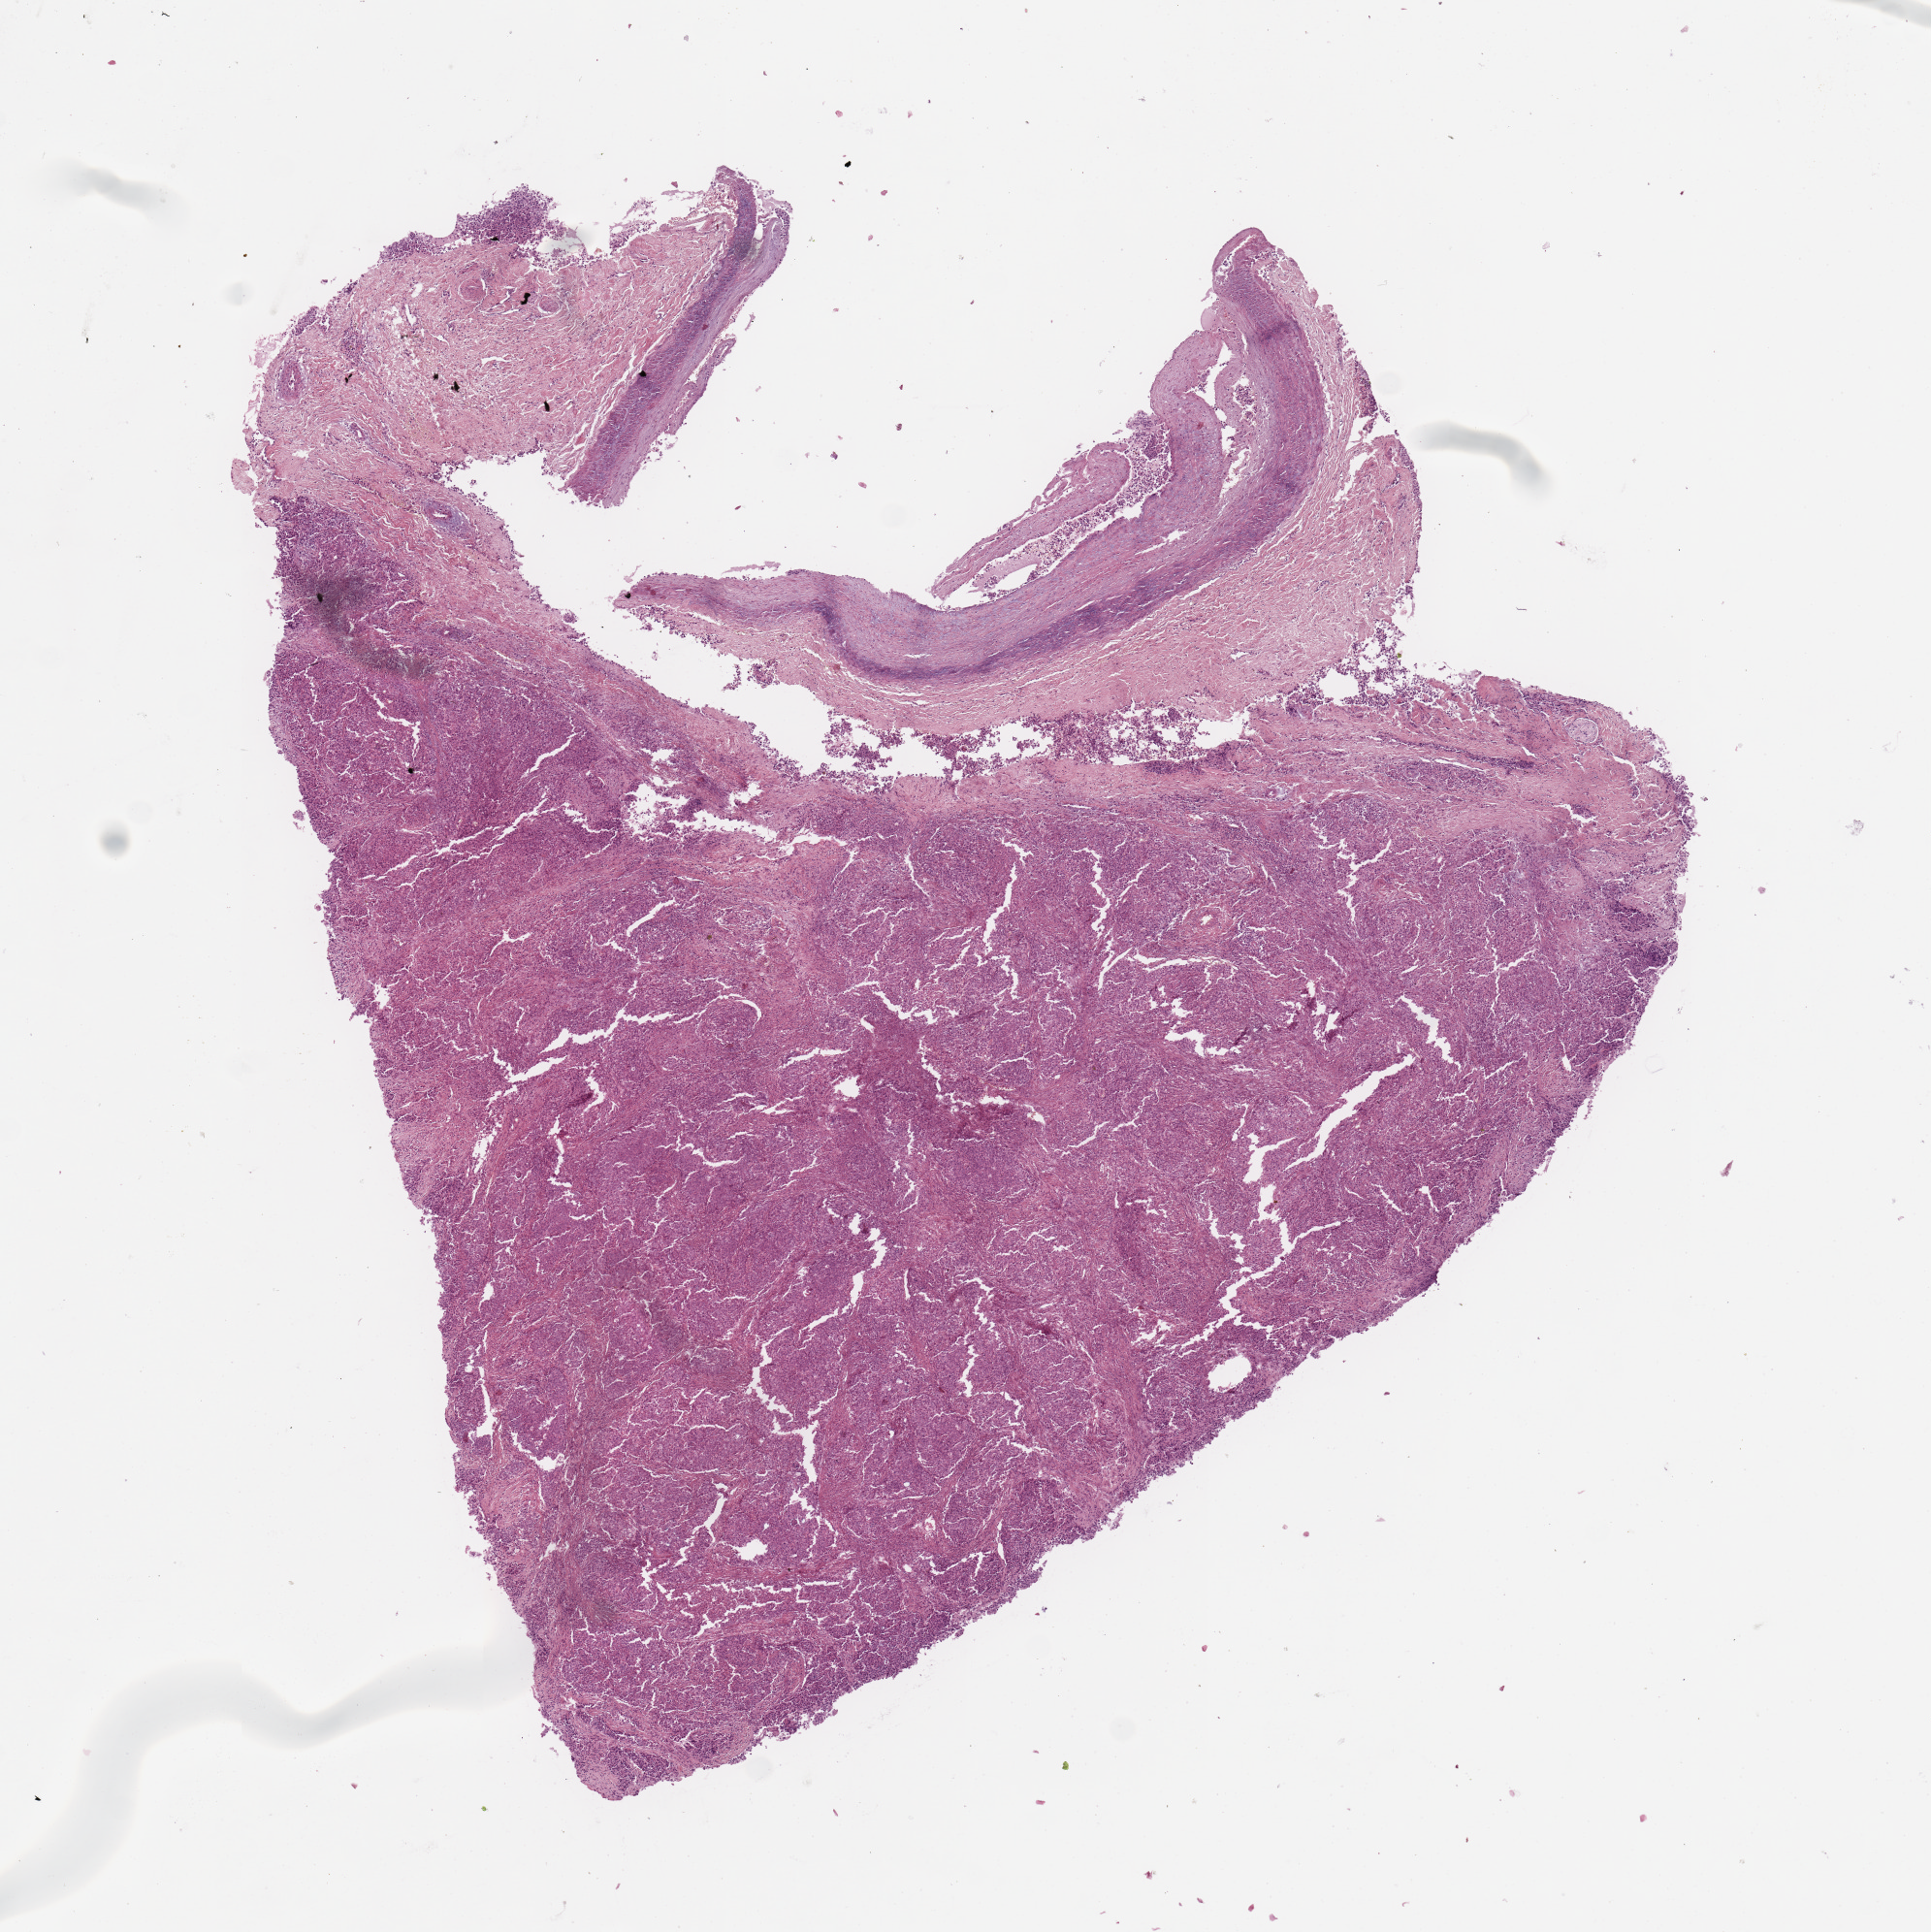
Whole-slide histology image, H&E, whole scanned area (about 7.9 x 7.9 mm, slide scanned at 20x) shown as a low-resolution overview; lung, tumour tissue. Male, 65 y/o.
Diagnosis: Squamous cell carcinoma, NOS.